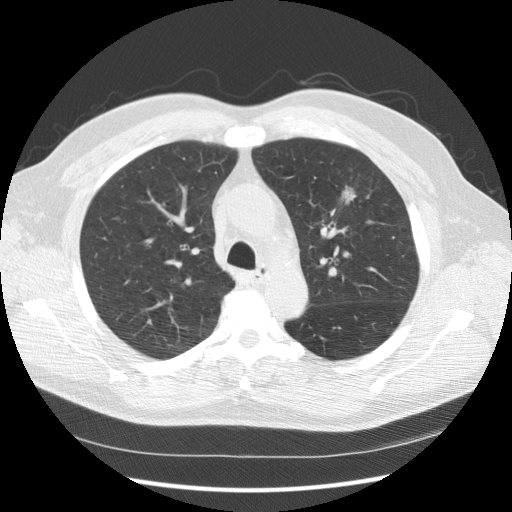
Low-dose screening chest CT, one axial slice; position 110 of 157 along the scan axis; reconstruction kernel STANDARD; 120 kVp; lung window (W 1500 / L -600 HU); 512 × 512 image matrix.
Outlined on this slice (outlined manually by an expert reader):
- lesion 1 (tumor, upper lobe of left lung): box from (x=342, y=187) to (x=355, y=204) px